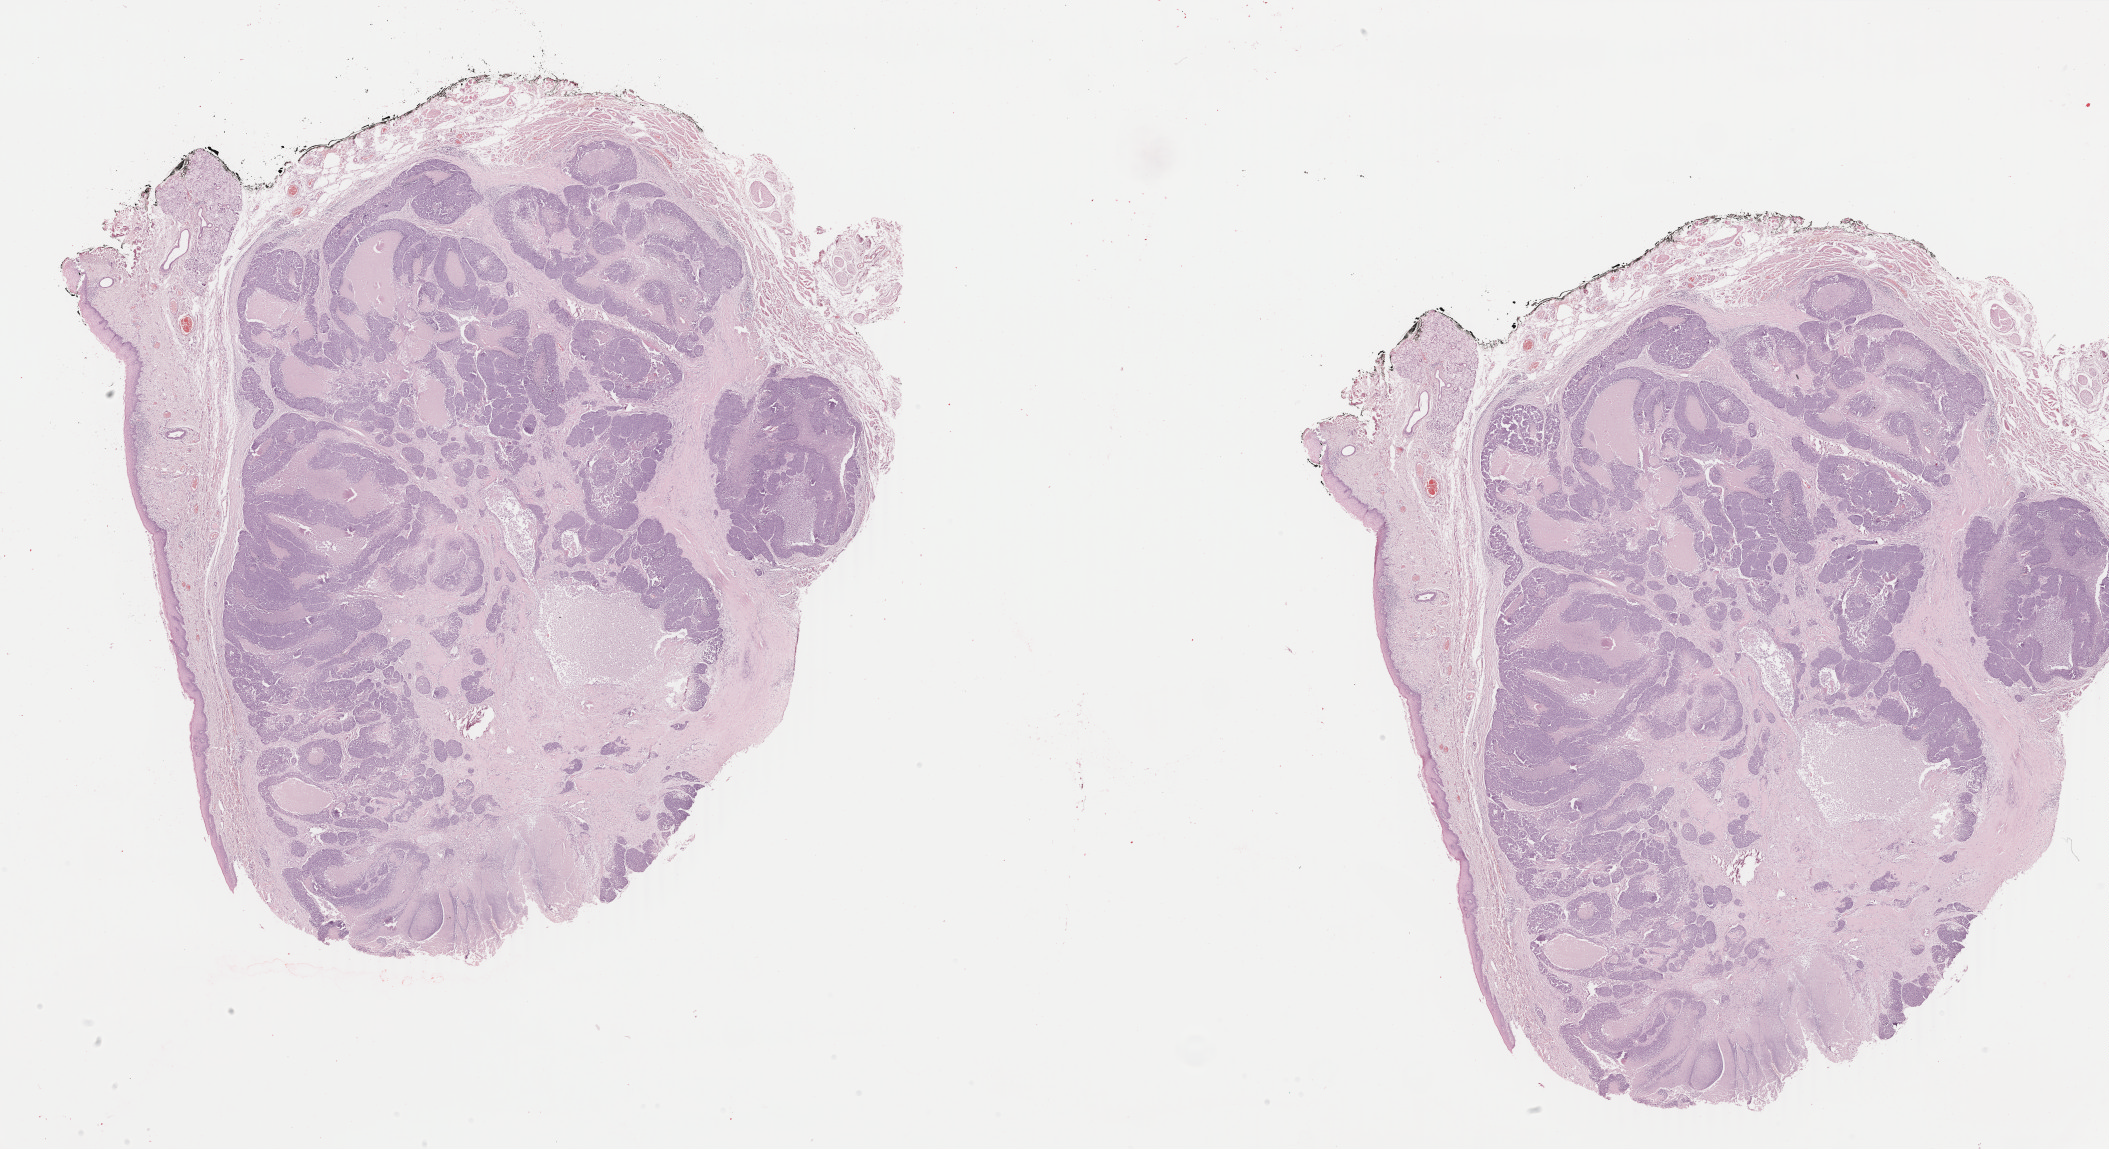
Whole-slide histology image, Hematoxylin and eosin (H&E) stained — shown as a low-resolution overview of the whole scanned area (about 33.6 x 18.3 mm, slide scanned at 40x); formalin-fixed paraffin-embedded (FFPE) diagnostic section; primary tumour sample from the head and neck. Female, age 55 years at initial diagnosis. Histologic grade: G3 (poorly differentiated).
Diagnosis: Squamous cell carcinoma, NOS. AJCC pathologic stage: I (7th edition). TNM: T1 N0.